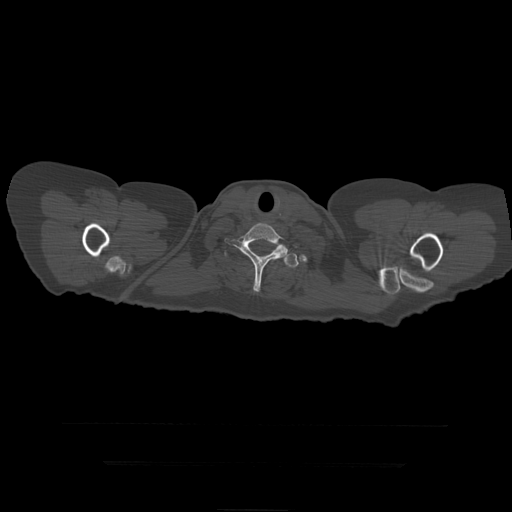
CT including the spine, one axial slice. Slice 386 of 399 in the series (ordered by position). Reconstruction kernel STANDARD. 120 kVp. Bone window (W 1800 / L 400 HU). 1.25 mm slice thickness. 512 × 512 image matrix, field of view 450 × 450 mm. Patient age 41 years. From the clinical record (not read from this slice): primary cancer: breast.
Structures marked on this image (semi-automatic segmentation, software-assisted and operator-edited):
- T1 vertebra: bounding box [x1, y1, x2, y2] px = [225, 223, 297, 292]
- T2 vertebra: [225, 253, 299, 268]